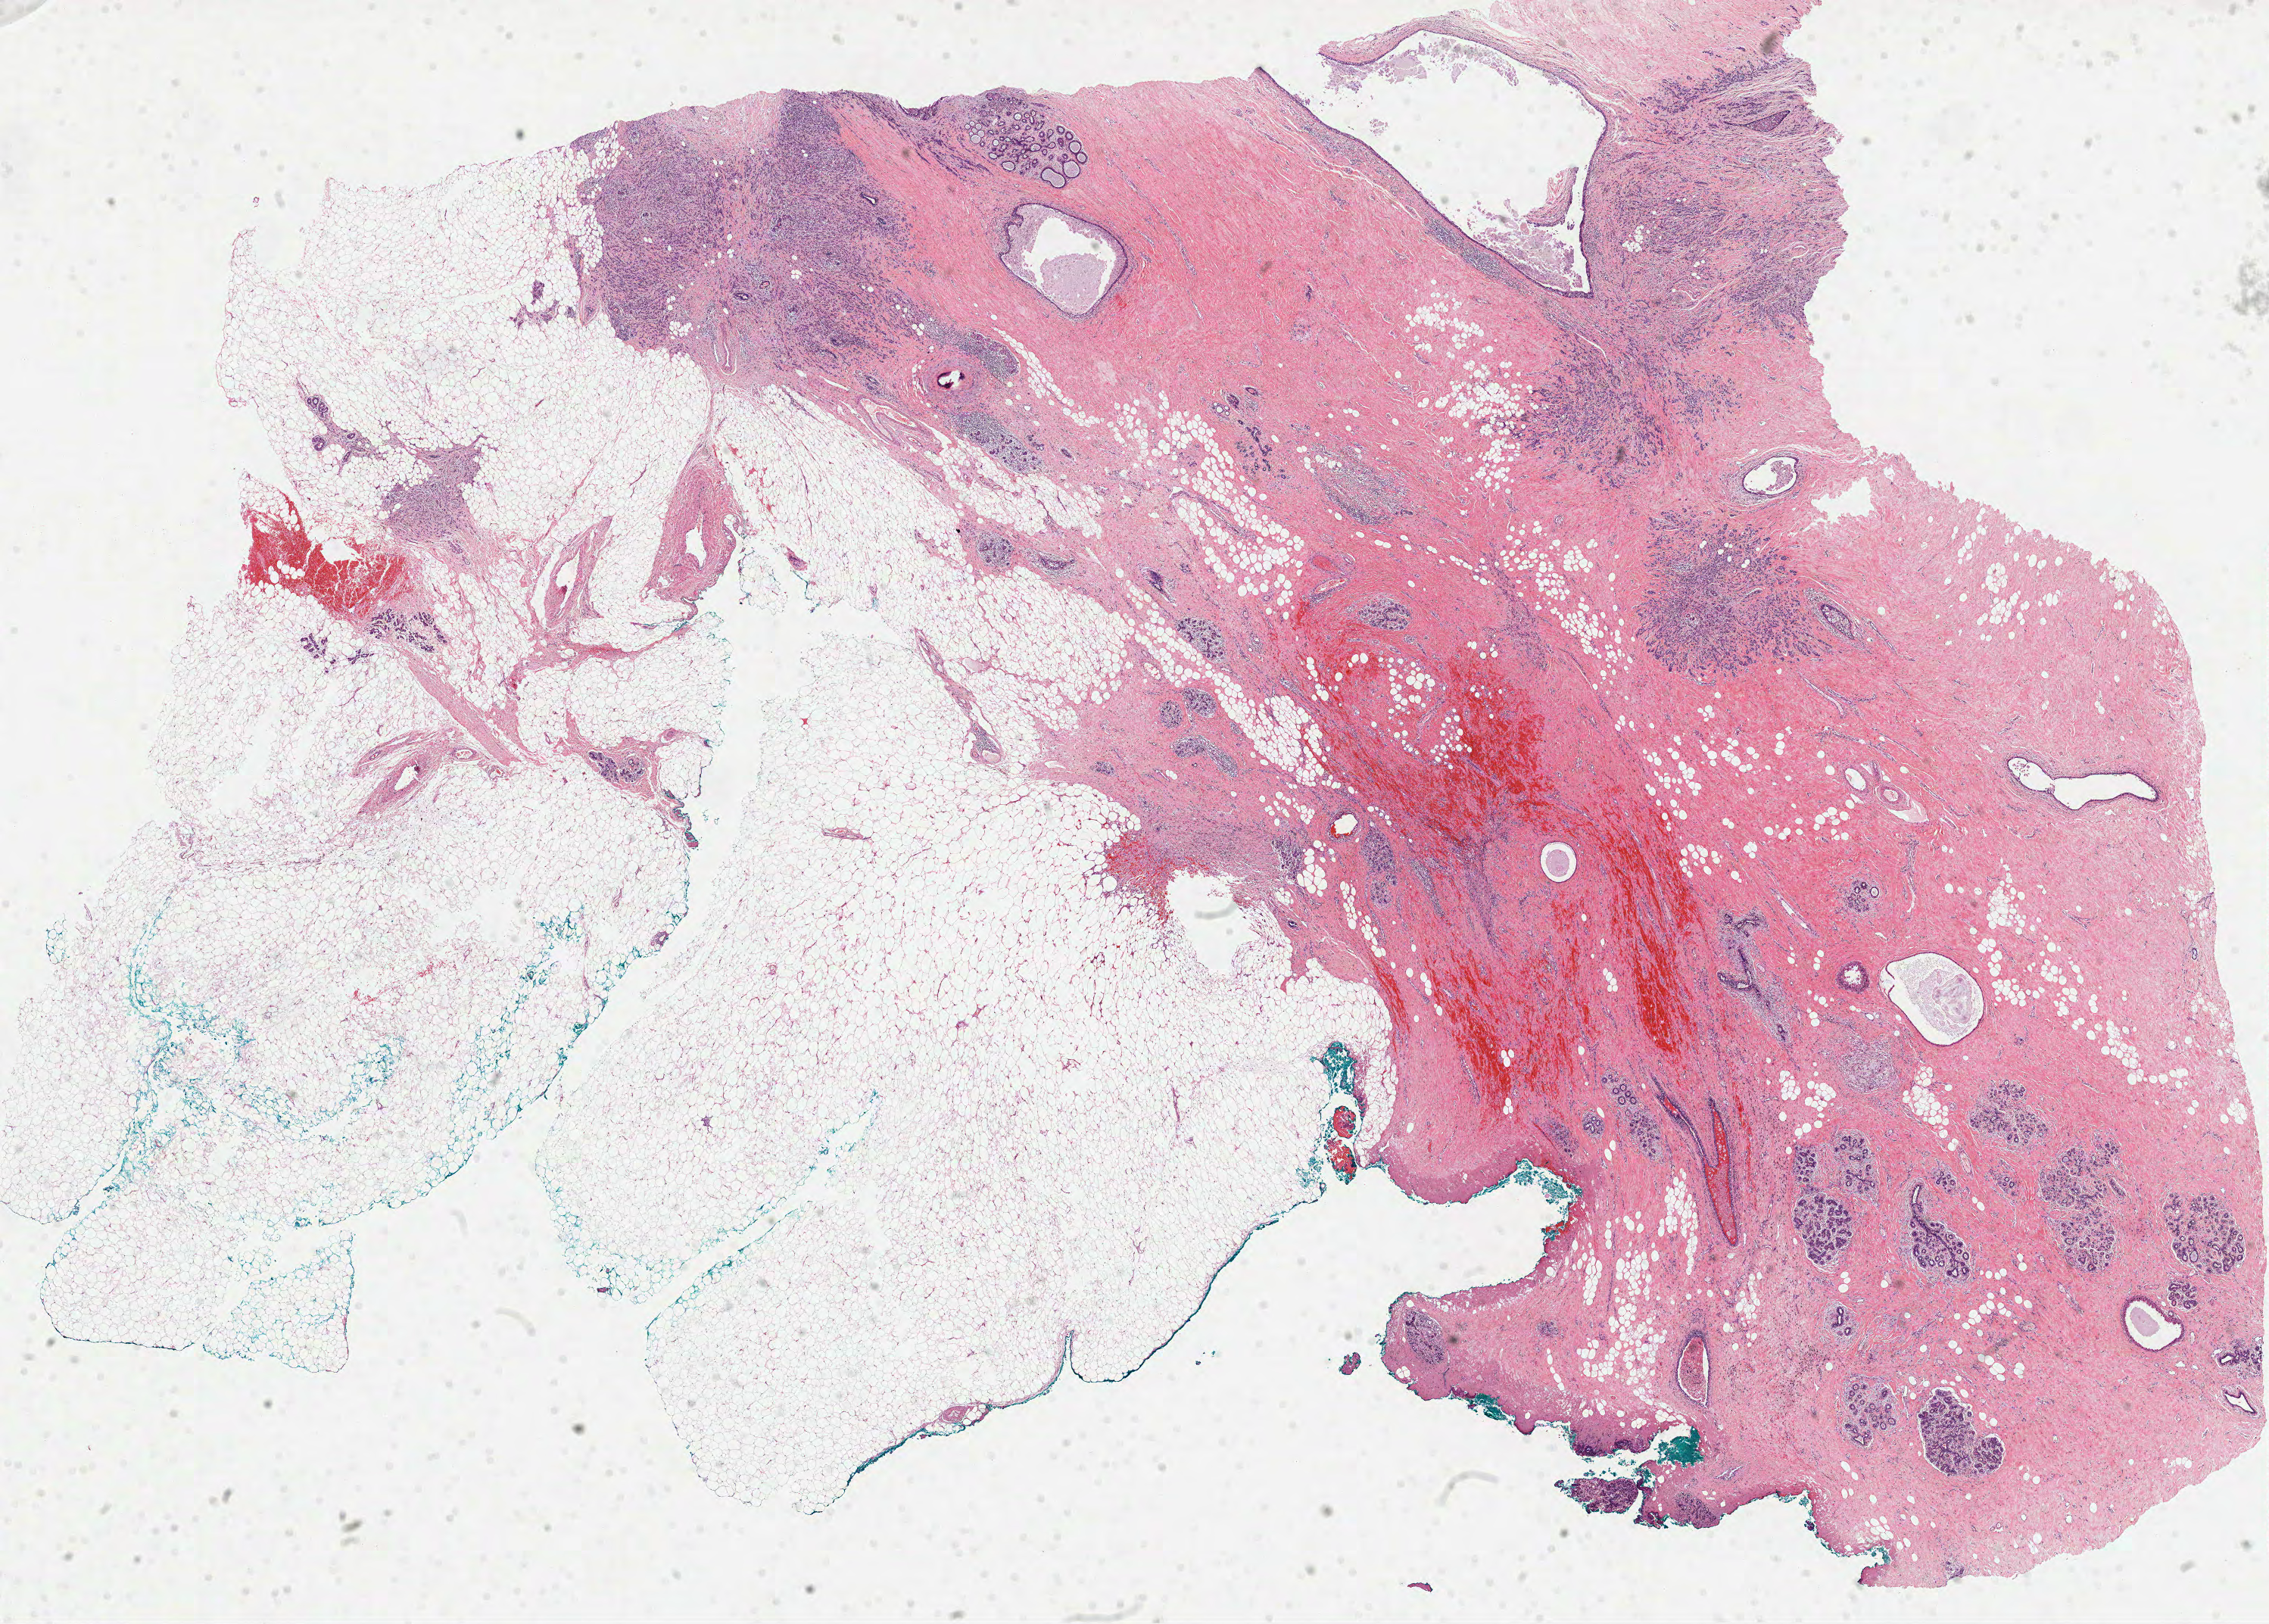
Digitized Hematoxylin and eosin (H&E) stained tissue section (whole slide) — low-resolution overview of the scanned area, about 24.2 x 17.3 mm (acquisition: 40x scan). Formalin-fixed paraffin-embedded (FFPE) diagnostic section. Breast, primary tumour sample. Patient: female, age at initial diagnosis 40 years.
AJCC pathologic stage: IIB. Pathologic diagnosis: Lobular carcinoma, NOS. Lymph nodes positive (case pathology): 3 of 7 examined. Laterality: right.